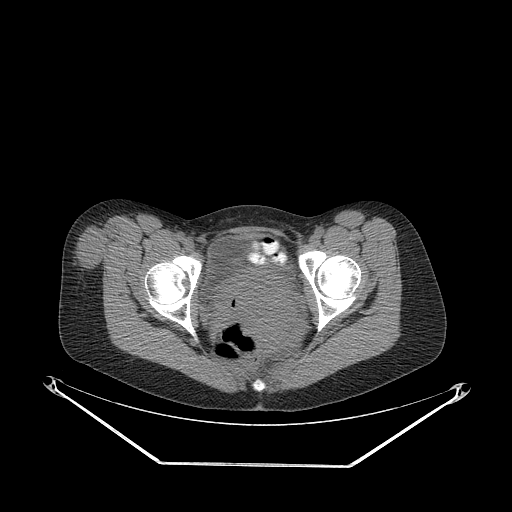
CT of an extremity soft-tissue mass (from a PET/CT study), one axial slice. 140 kVp. Soft-tissue window (W 400 / L 40 HU). 3.75 mm slice thickness. 512 × 512 image matrix, field of view 500 × 500 mm. Female patient. Case-level facts recorded for this patient, not image findings: histological type: synovial sarcoma; grade: intermediate; site of the primary tumour: right thigh.
Structures marked on this image (expert contour drawn on MRI and transferred to this co-registered scan by the dataset authors):
- gross tumour volume including surrounding oedema: bounding box <73,224,118,273> (left, top, right, bottom; pixels)
- gross tumour volume (mass): <75,226,118,273>